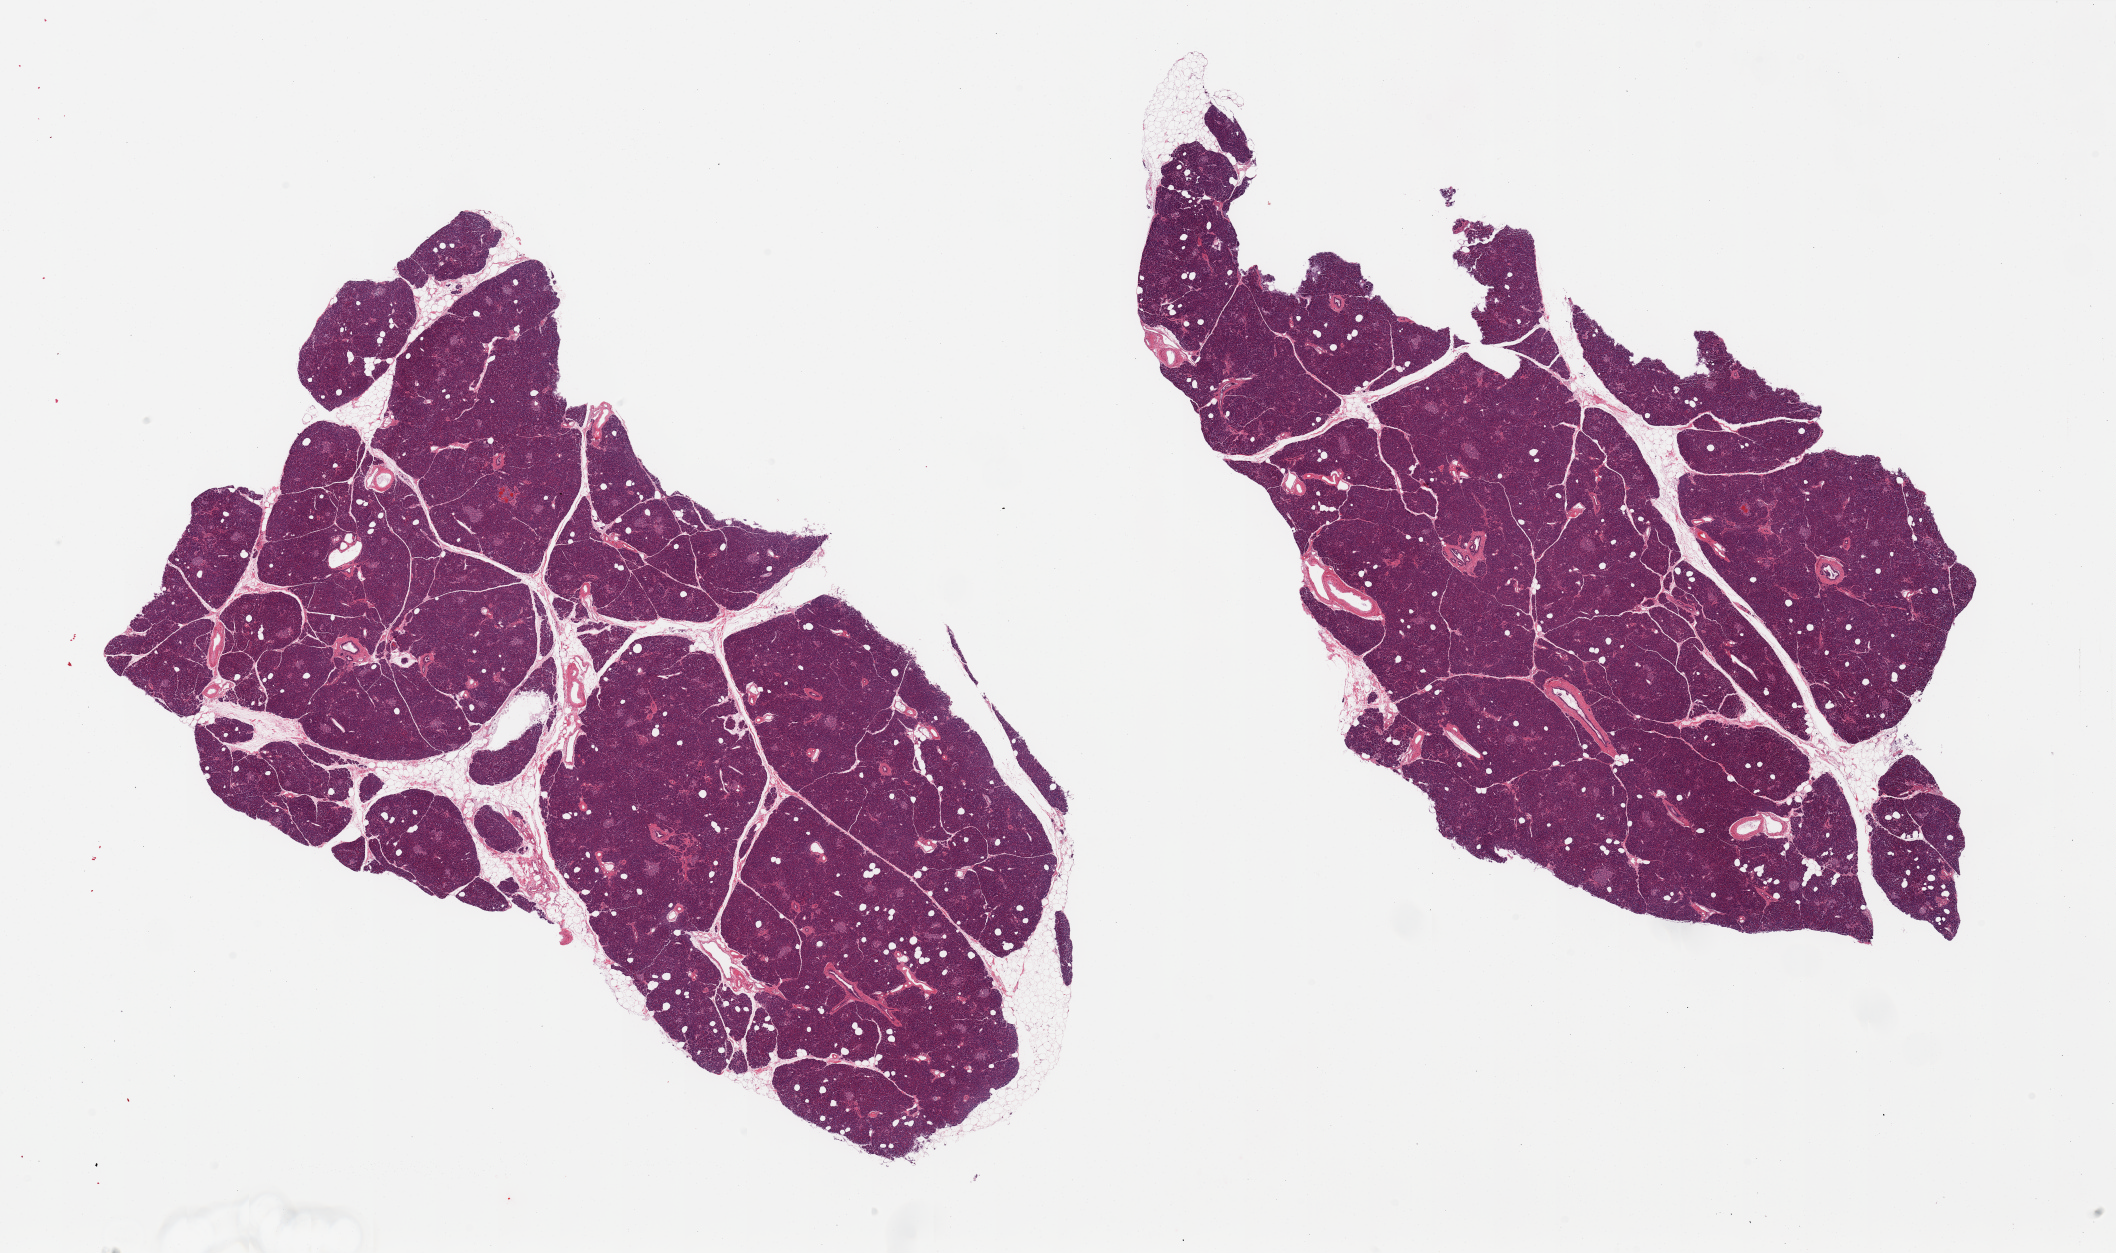
Digitized H&E-stained section, a low-resolution overview of the entire scanned area, about 33.5 x 19.8 mm. PAXgene-fixed, paraffin-embedded tissue. Target tissue: pancreas. Tissue donor sample.
Pathologist's review note for this sample: 2 pieces, well preserved; Islets well visualized; Trace adherent fat; good specimens.